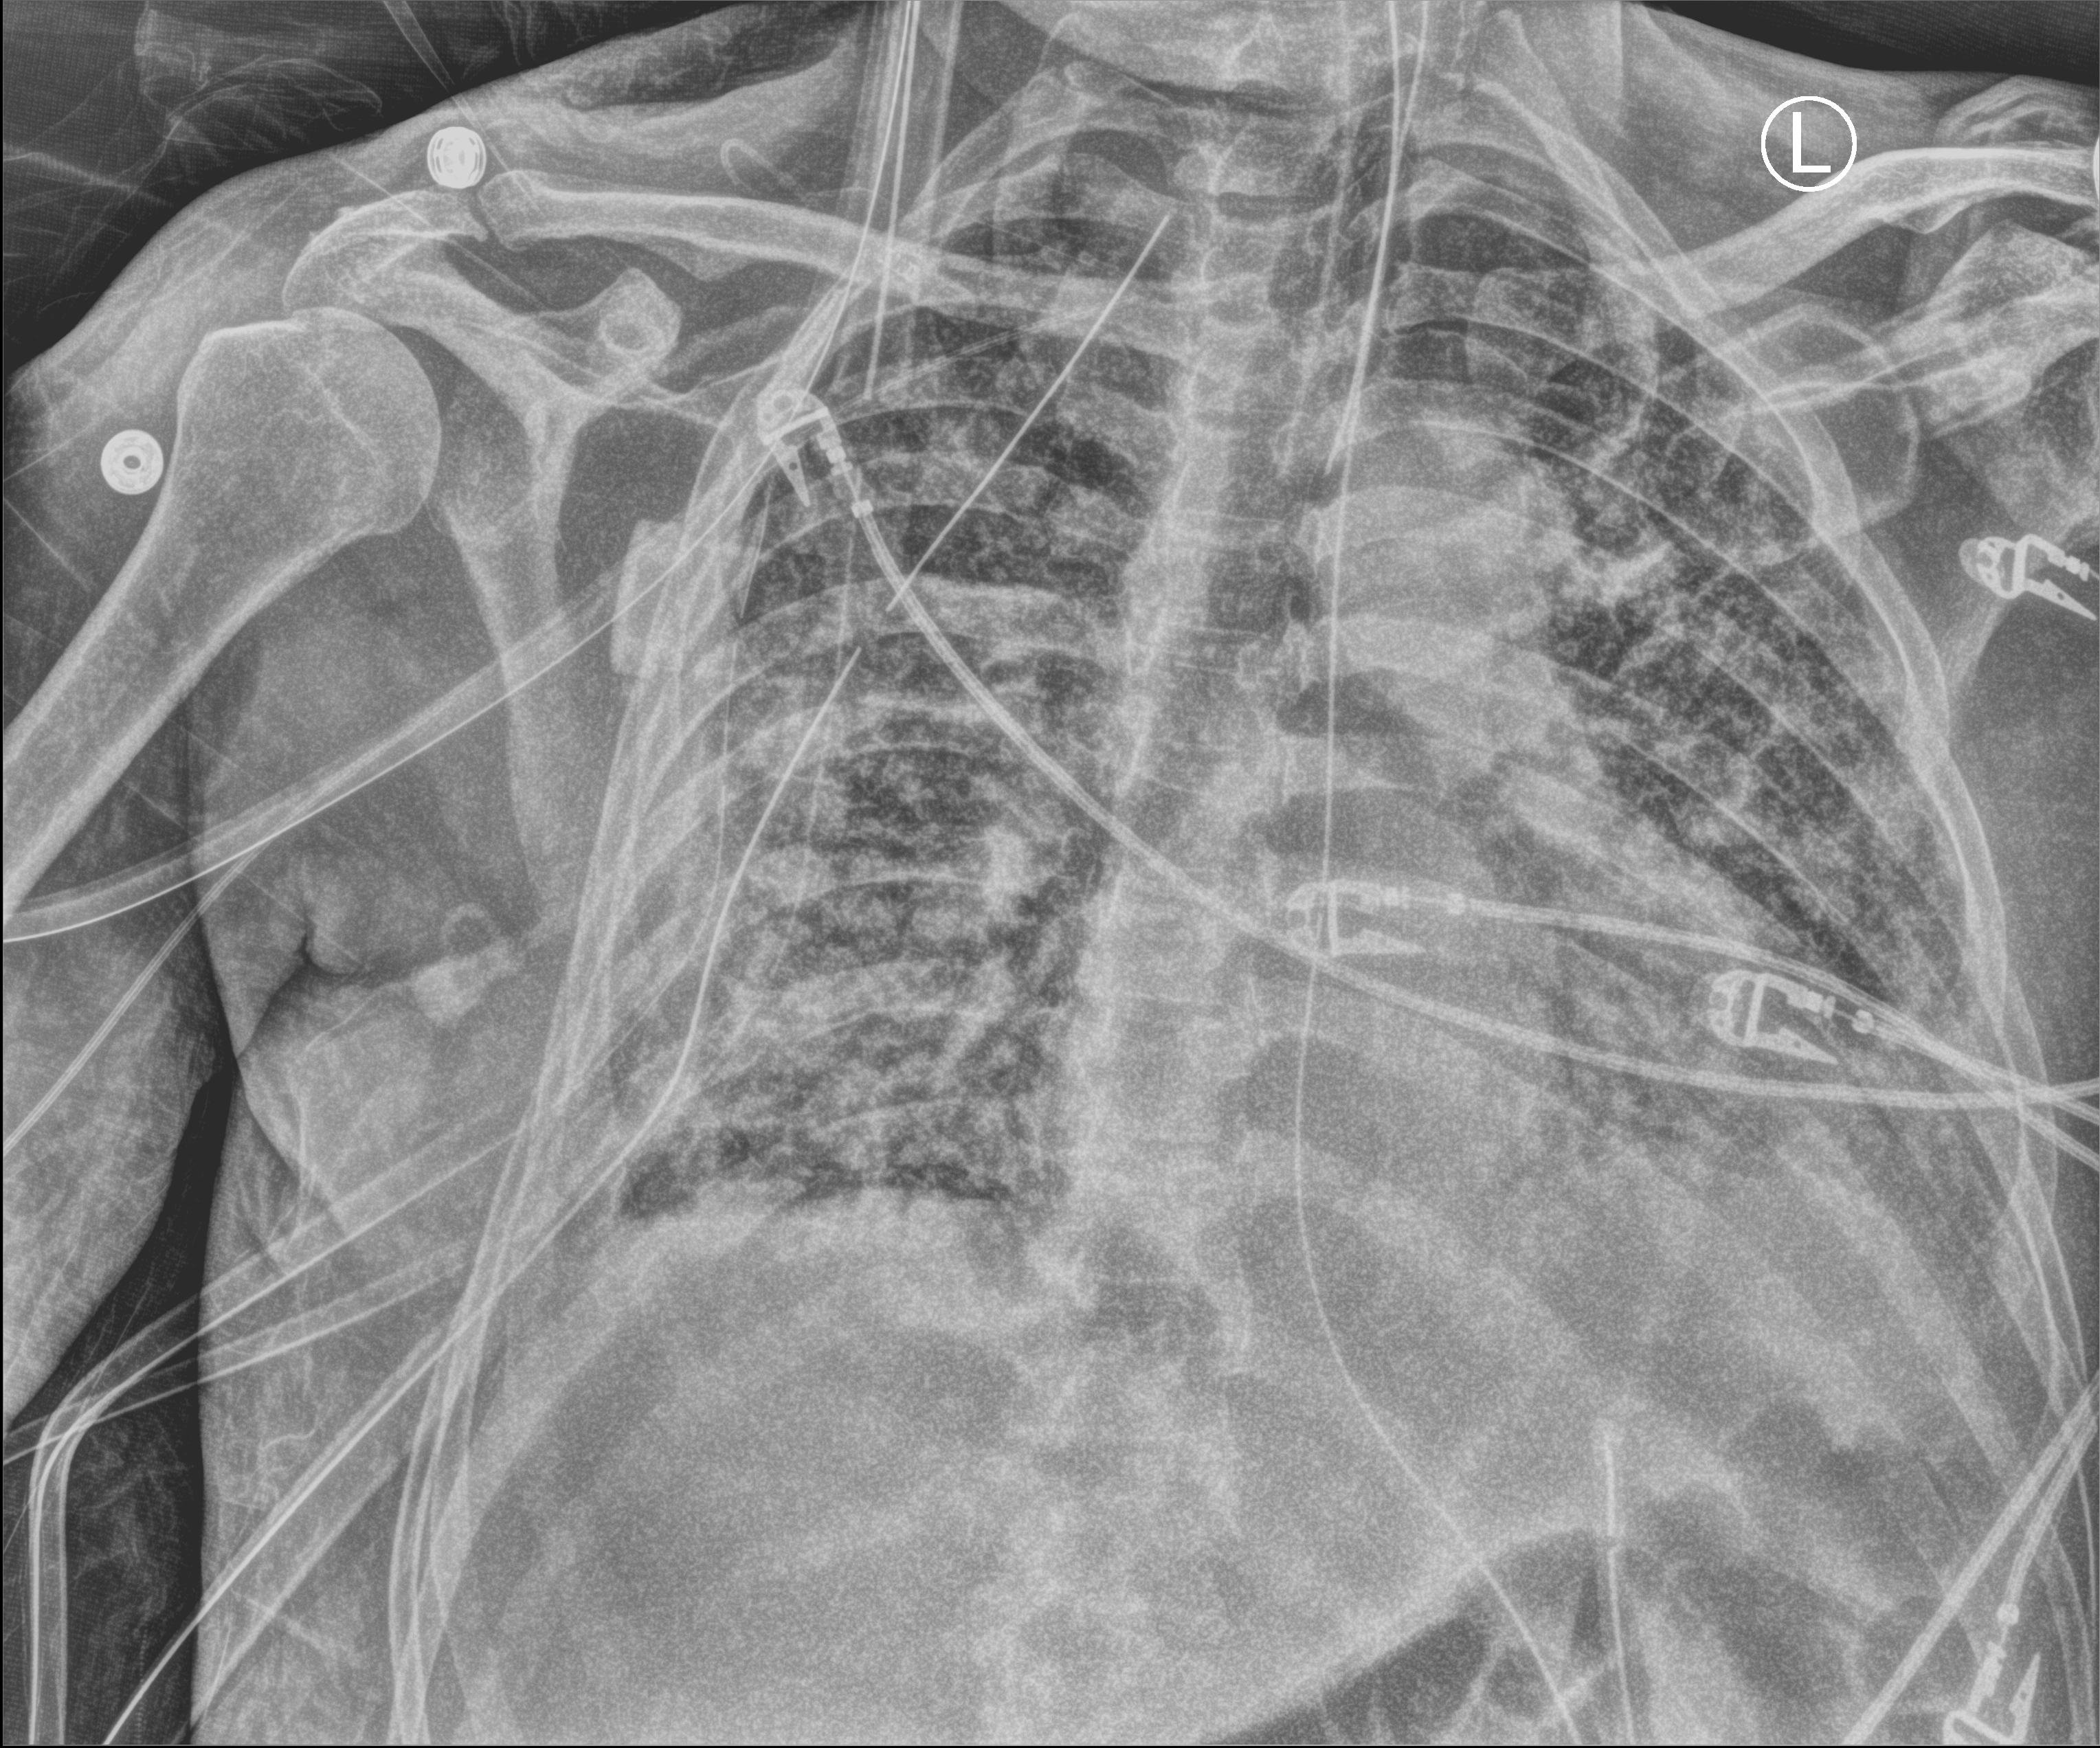
Portable chest radiograph, anteroposterior (AP) projection. Male patient hospitalised with COVID-19, age 60–74 years.
Admission-level facts for this patient (not findings on this image; timing relative to this image not recorded): mechanically ventilated during this hospital stay: yes.